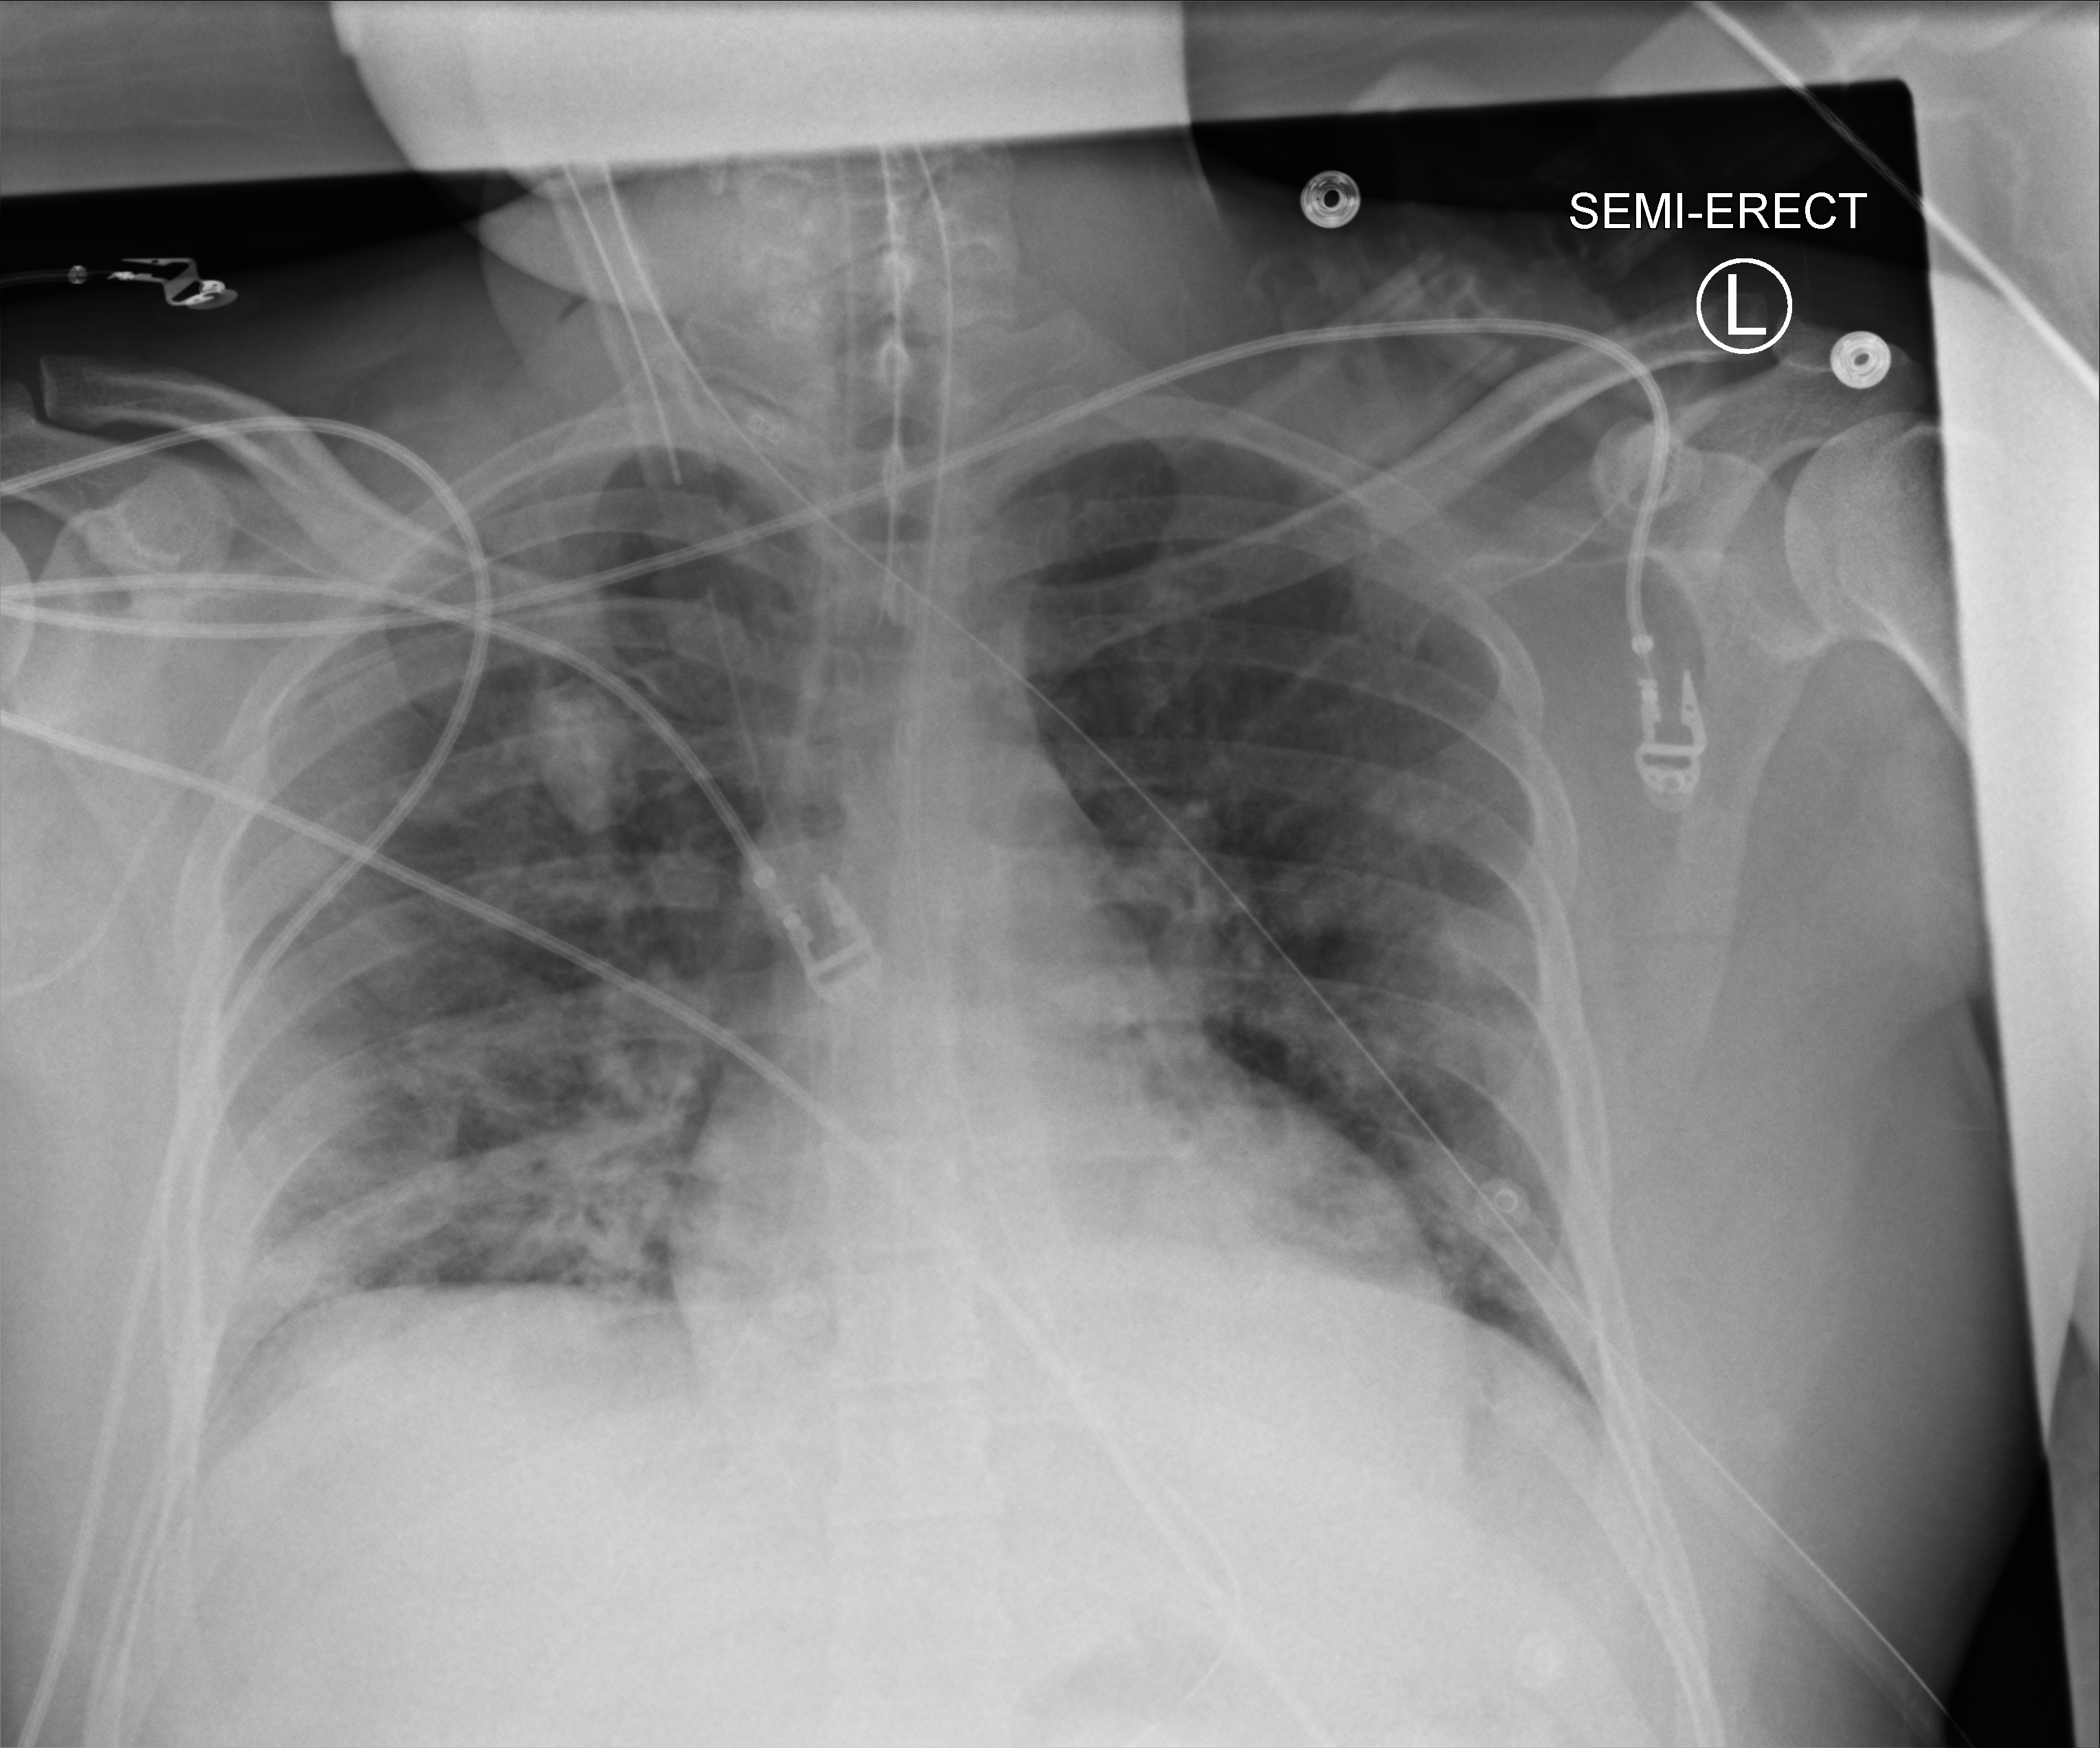
Bedside chest radiograph (computed radiography), anteroposterior (AP) projection. Patient hospitalised with COVID-19; male, aged 18–59 years.
Admission-level facts for this patient (not findings on this image; timing relative to this image not recorded): chronic kidney disease (admission record): no; mechanically ventilated during this hospital stay: yes.